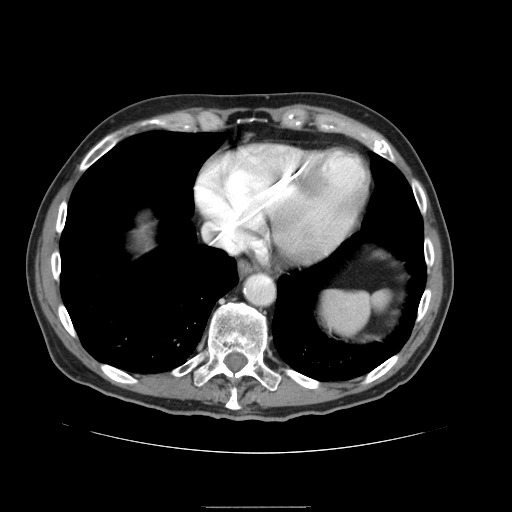
Contrast-enhanced abdominal CT, one axial slice; position 139 of 168 along the scan axis; 120 kVp; soft-tissue window (W 400 / L 40 HU); 512 × 512 image matrix. Male patient, age 74 years. Case-level facts recorded for this patient, not image findings: diagnosis: colorectal cancer liver metastases, imaged before liver resection; multiple liver metastases: no; largest metastasis: 14.5 cm; disease in both lobes: yes.
Outlined on this slice (expert manual segmentation):
- liver: bounding box <125,208,156,256> (left, top, right, bottom; pixels)
- planned liver remnant (the part of the liver to remain after resection): <124,207,158,259>